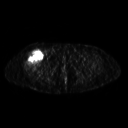
FDG PET of an extremity soft-tissue mass (from a PET/CT study), one axial slice. Position 277 of 311 along the scan axis. 128 × 128 image matrix, field of view 500 × 500 mm. Female patient, age 57 years. From the clinical record (not read from this slice): histological type: pleiomorphic undifferentiated sarcoma; grade: high; site of the primary tumour: right quadricep.
Annotated regions visible in this slice (expert contour drawn on MRI and transferred to this co-registered scan by the dataset authors):
- tumour plus oedema (research contour): bounding box [x1, y1, x2, y2] px = [24, 49, 43, 68]
- tumour (research contour): [24, 49, 43, 68]